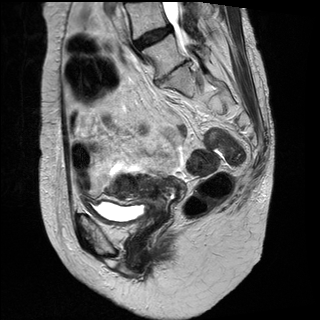
Pelvic MRI for cervical cancer, one sagittal slice; position 13 of 31 along the scan axis; T2-weighted; 1.5 T; TE 89 ms, TR 3890 ms; 4 mm slice thickness; 320 × 320 image matrix, field of view 260 × 260 mm. Female patient, age 61 years.
Structures marked on this image (expert manual segmentation):
- uterus and cervix: bounding box <106,172,187,215> (left, top, right, bottom; pixels)